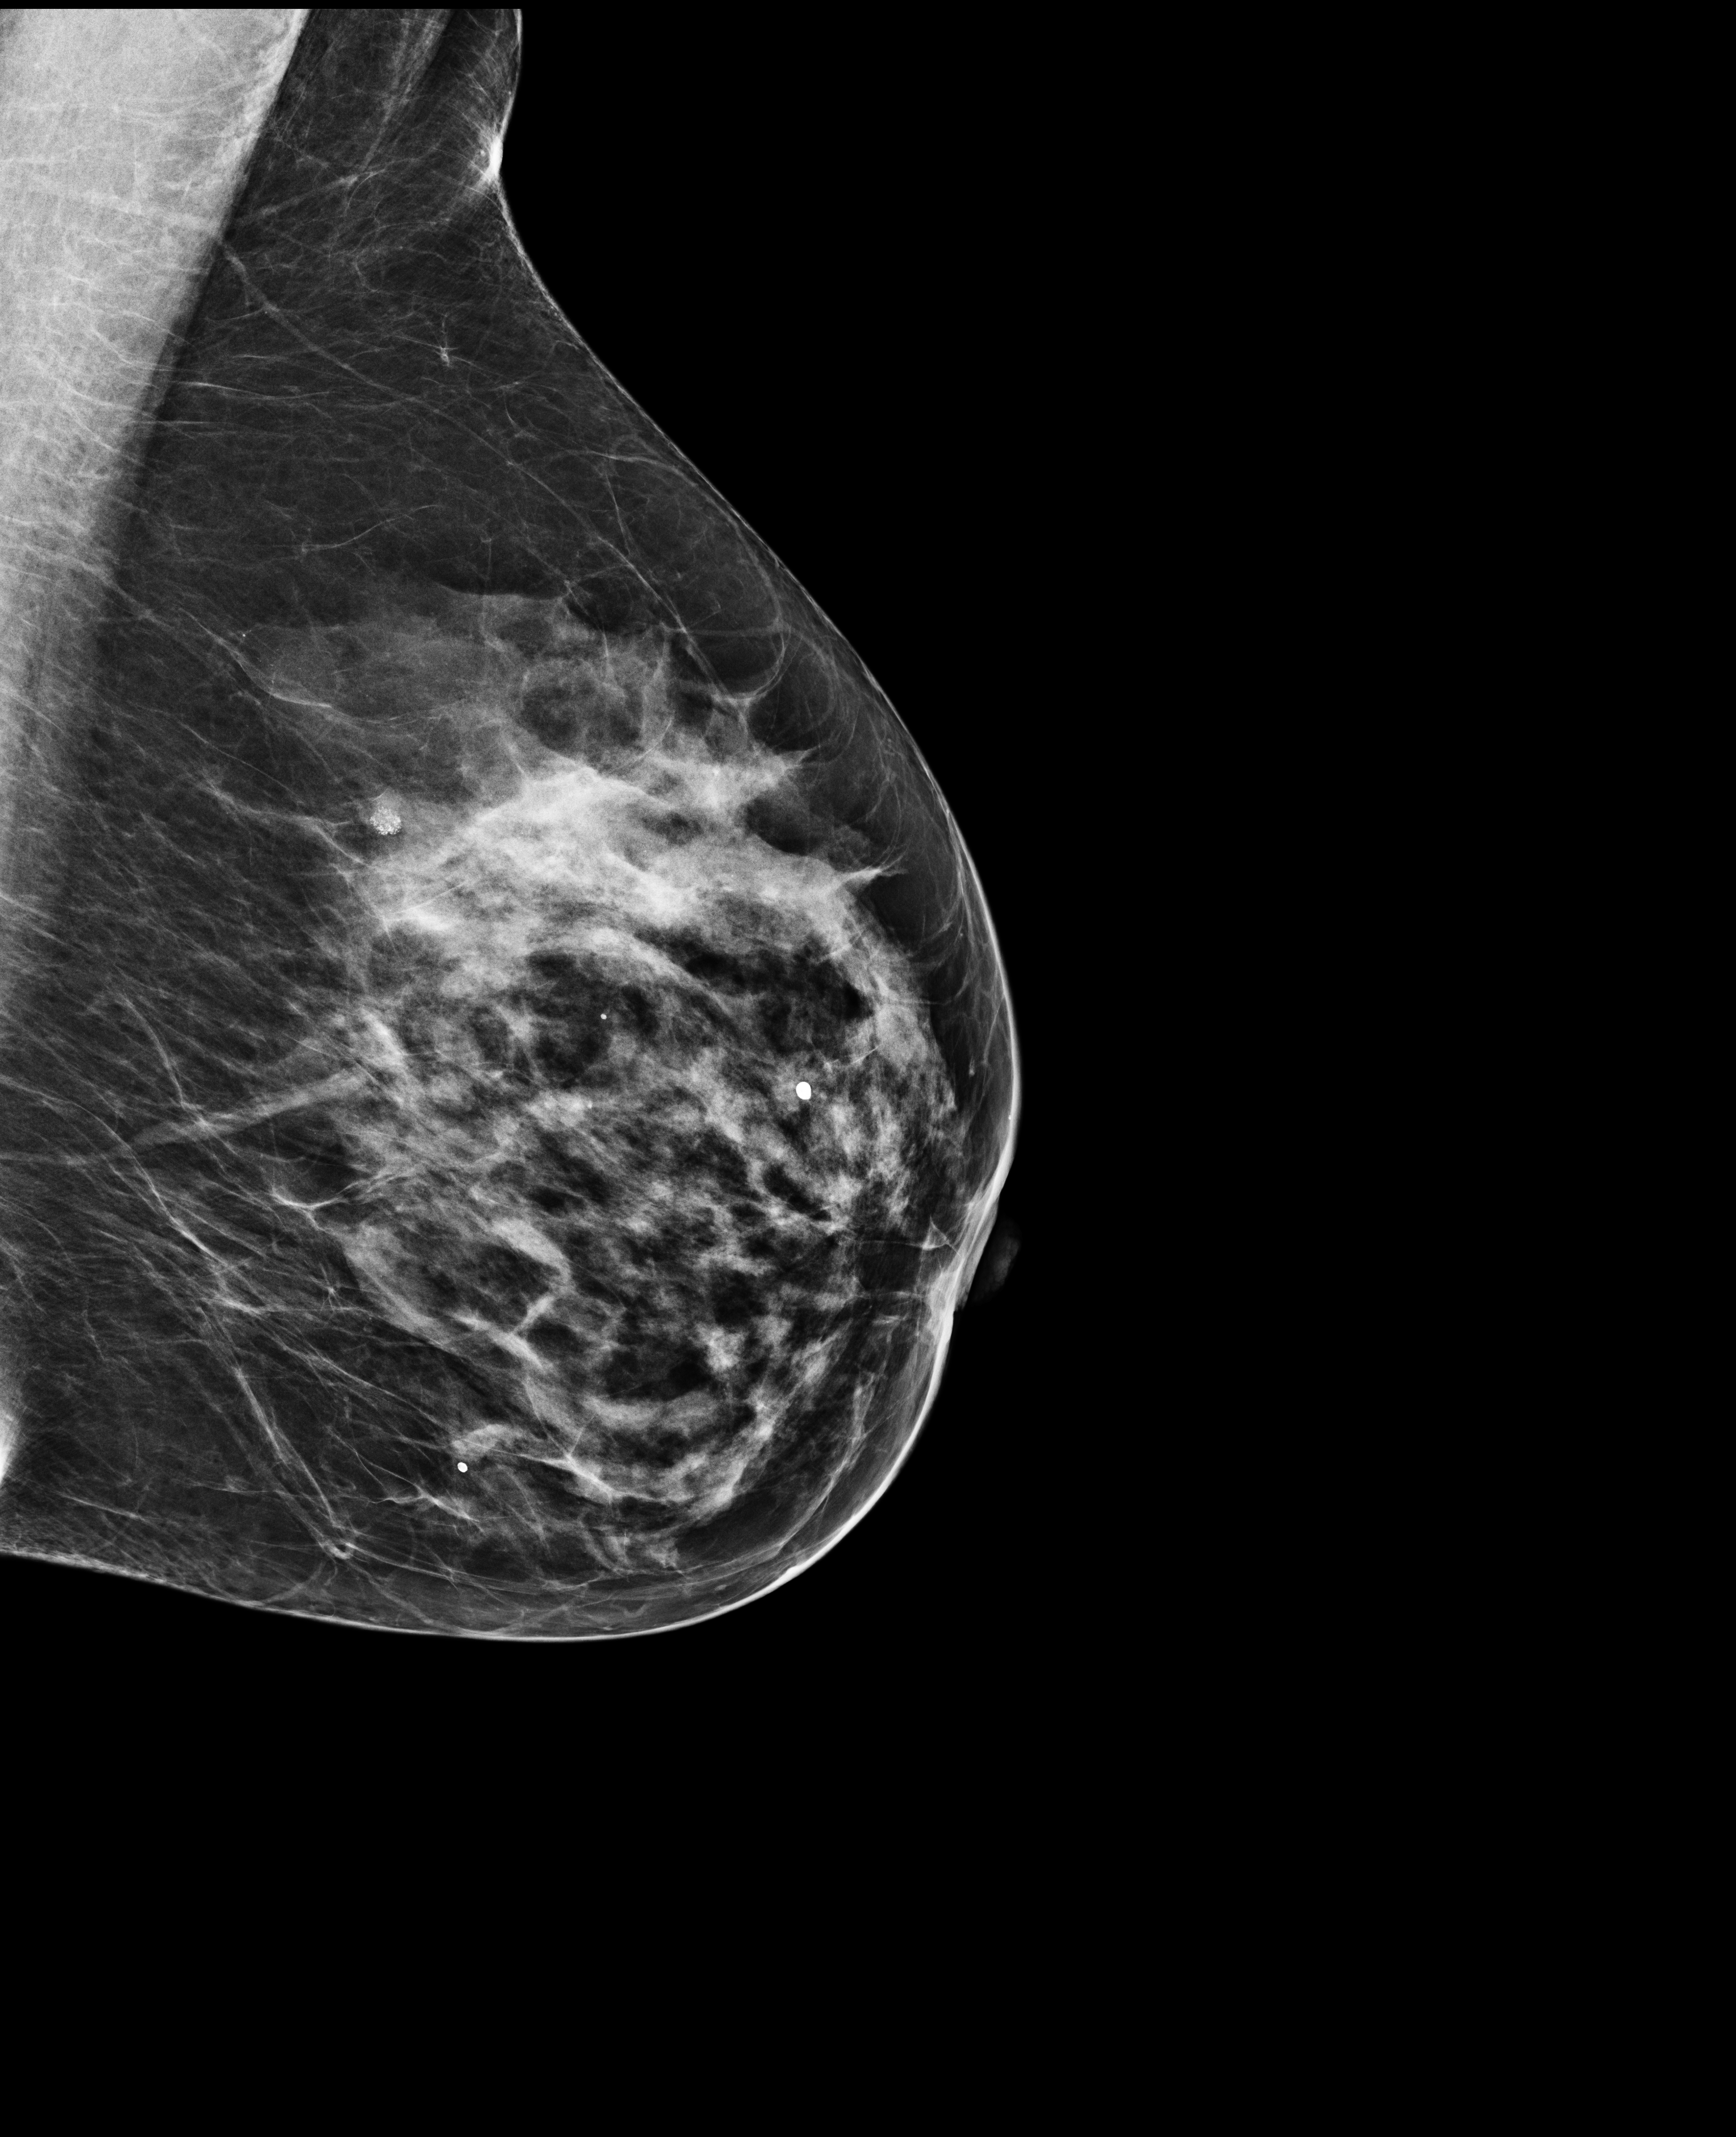
Full-field digital mammogram (FFDM); left breast; medio-lateral oblique projection; annual screening mammography examination; system: Selenia Dimensions. Patient aged 62 years (female).
BI-RADS breast density category at the screening exam (both breasts, scale 1–4): 3. Final BI-RADS category for the screening round (tomosynthesis exam, both breasts): category 2. Recall: no recall after this screen.